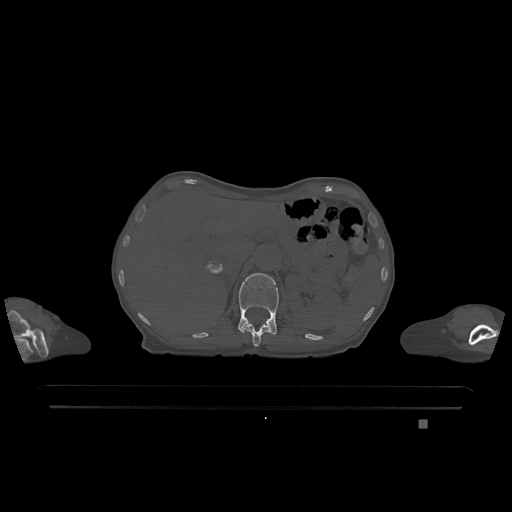
CT including the spine, one axial slice. Position 497 of 1317 along the scan axis. Bone window (W 1800 / L 400 HU). 512 × 512 image matrix. Patient: female, 74 years. Case-level facts recorded for this patient, not image findings: primary cancer: lung; vertebrae with lytic lesions (as recorded): T1, T4, T5, T6, L4, L5.
Annotated regions visible in this slice (semi-automatically segmented with operator editing):
- L1 vertebra: box from (x=238, y=273) to (x=279, y=335) px
- T12 vertebra: (x=242, y=324)–(x=270, y=347)